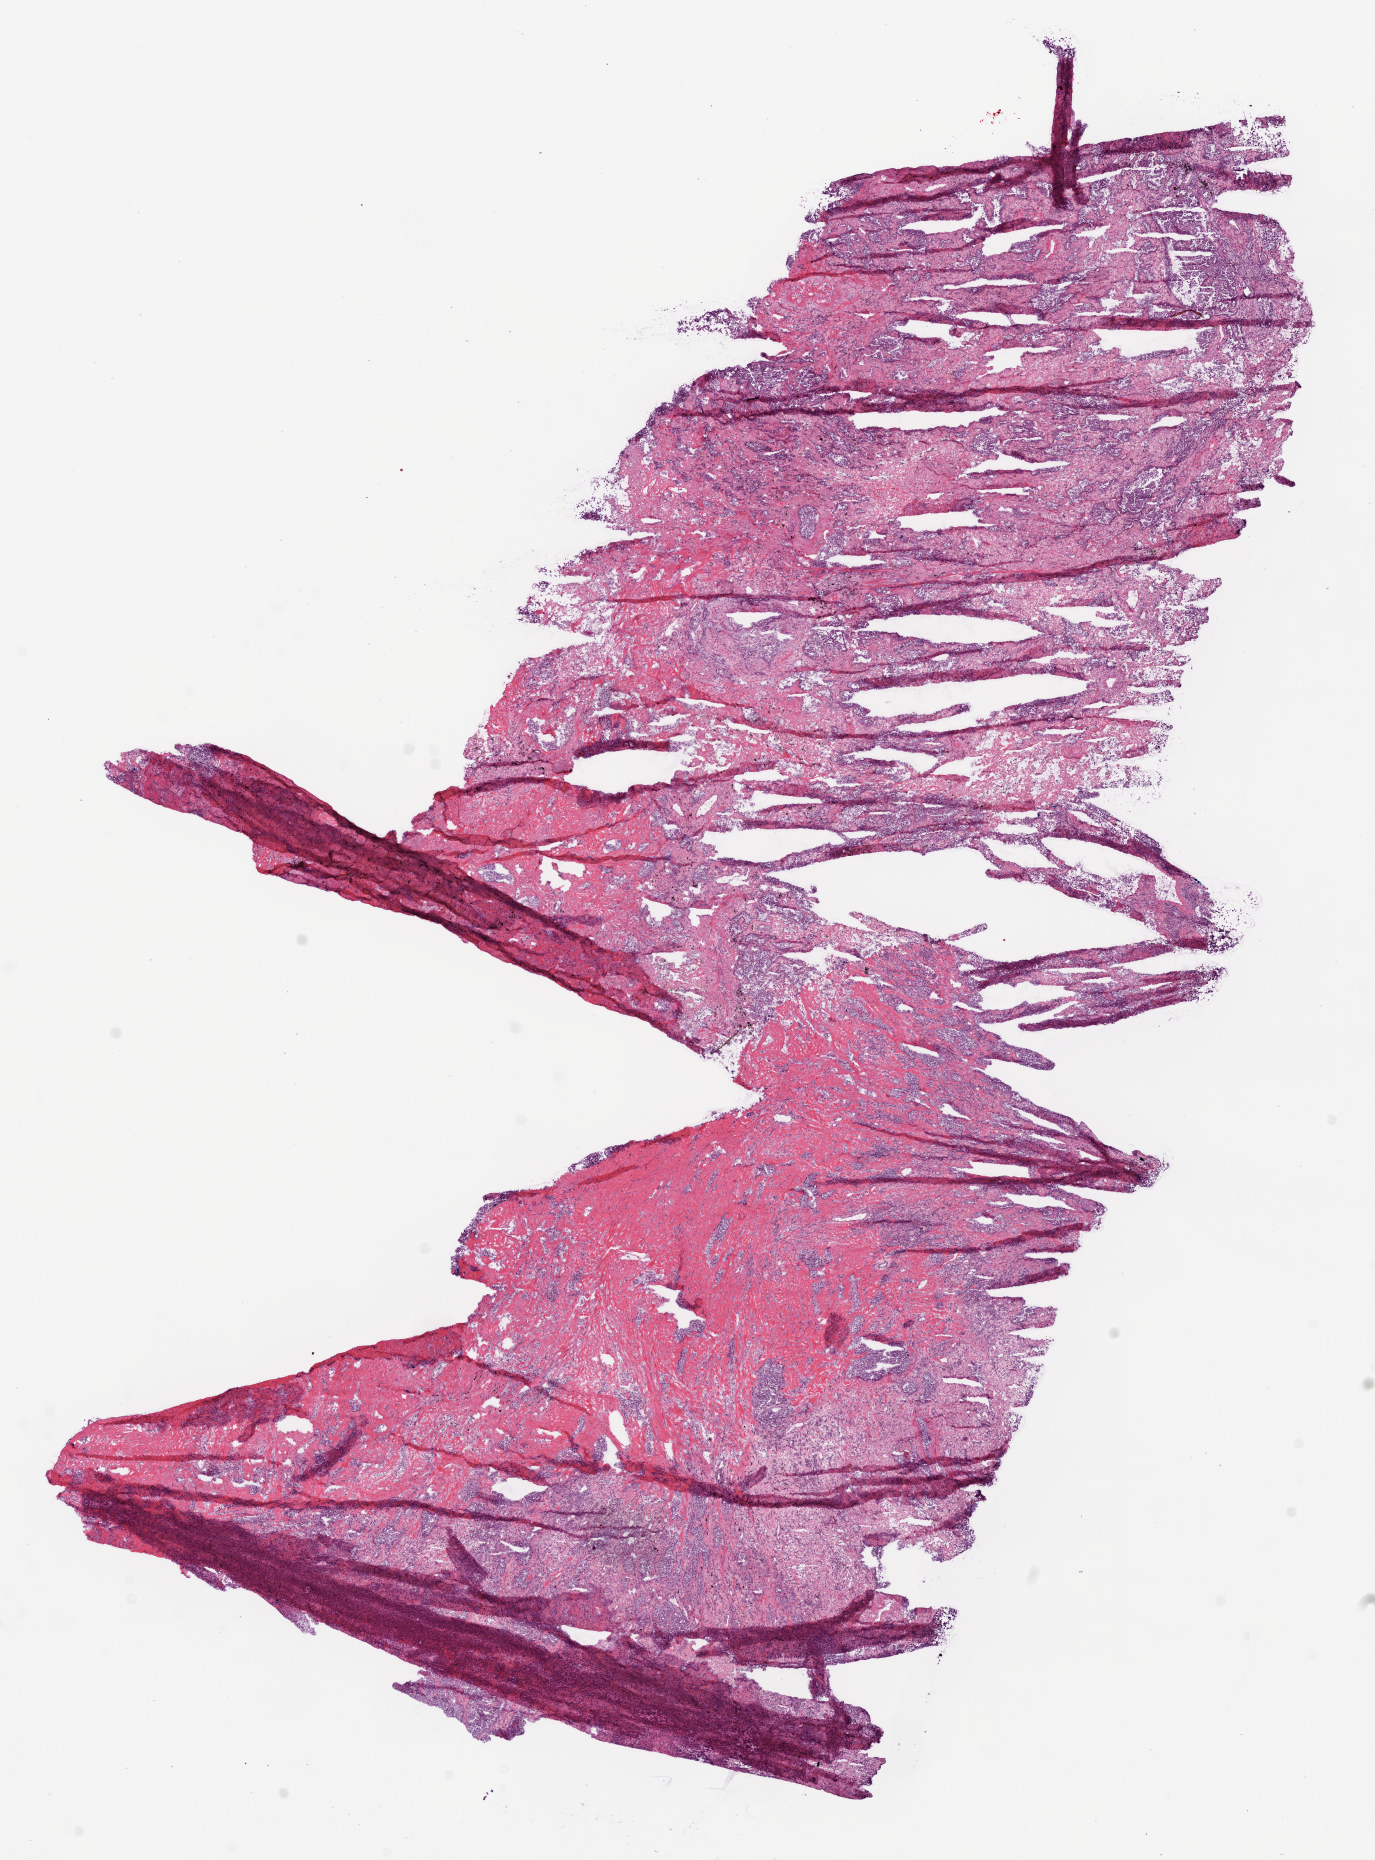
H&E whole-slide image, shown as a low-resolution overview of the whole scanned area (about 11.0 x 14.9 mm, acquisition: 20x scan). Frozen section. Lung, primary tumour sample. Patient: female, age at initial diagnosis 60 years. Composition of this section per pathologist review: tumour cells 55%, tumour nuclei 80%, normal cells 0%, stromal cells 40%, necrosis 5%.
• laterality: right
• diagnosis: Adenocarcinoma, NOS
• AJCC pathologic stage: IB